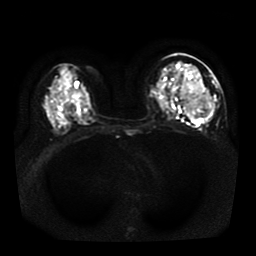
Breast MRI, one axial slice. Diffusion-weighted series; image 2 of 4 stored at this slice position (different b-values; order by instance number). 1.5 T. 256 × 256 image matrix. Female patient.
Structures marked on this image (expert manual segmentation):
- tumour on diffusion-weighted imaging: bounding box [x1, y1, x2, y2] px = [180, 82, 212, 117]